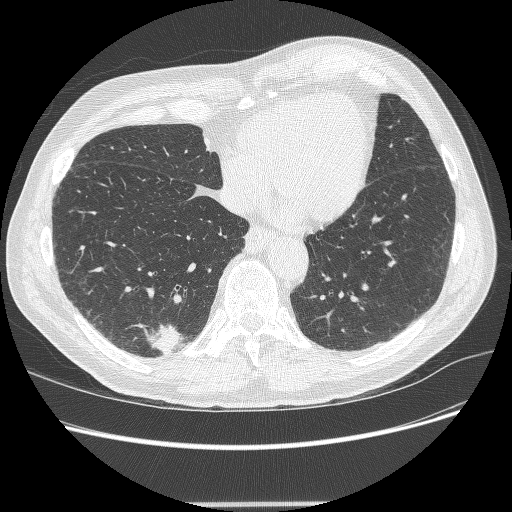
Low-dose screening chest CT, axial slice; second annual screen; lung window (W 1500 / L -600 HU); 1.25 mm slice thickness; 120 kVp; slice 72 of 245 in the series; 512 × 512 image matrix. Male, age 71 years at enrolment.
• Lesion marked by an expert reader, box from (x=137, y=322) to (x=189, y=363) px.
• The screening reader recorded 5 non-calcified nodules or masses ≥4 mm on this exam (right lower lobe, right lower lobe, right upper lobe, right upper lobe, right upper lobe); which of them this box marks is not recorded.
• Official screen result: positive, change unspecified: nodule(s) >= 4 mm or enlarging nodule(s), mass(es), or other non-specific abnormalities suspicious for lung cancer.
• Participant outcome: lung cancer diagnosed 7 days after this screen — squamous cell carcinoma, NOS, right lower lobe, moderately differentiated (G2), stage IA (AJCC 6th edition), 27 mm at pathology.